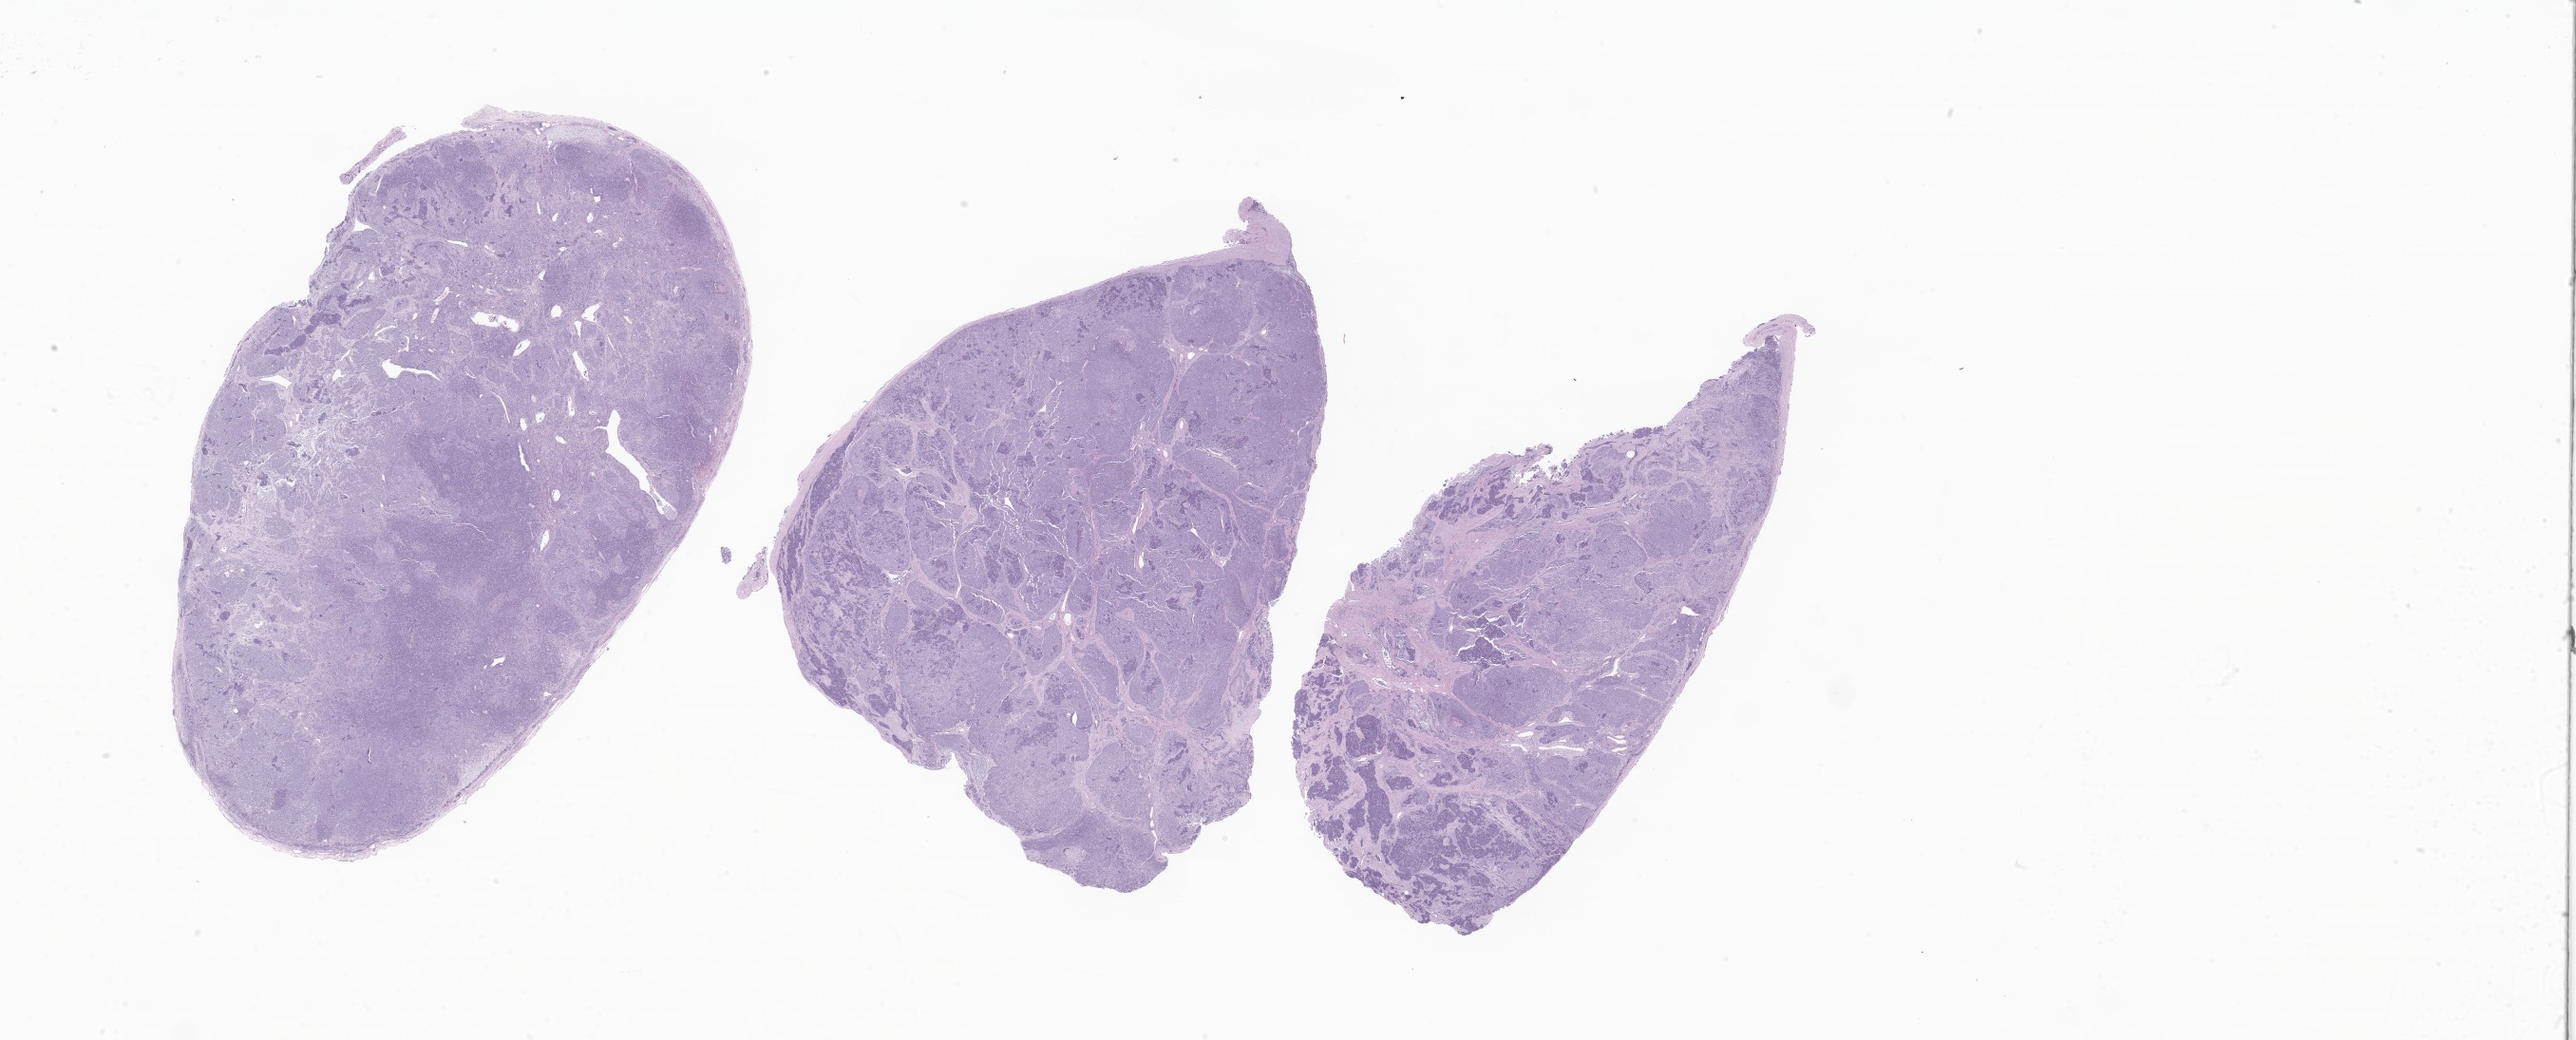
Hematoxylin and eosin (H&E) whole-slide image of tumor tissue from the head and neck, low-resolution overview of the scanned area, about 45.8 x 18.5 mm; FFPE section. Female patient, age 141 months (11 years 9 months).
* diagnosis: Rhabdomyosarcoma, NOS